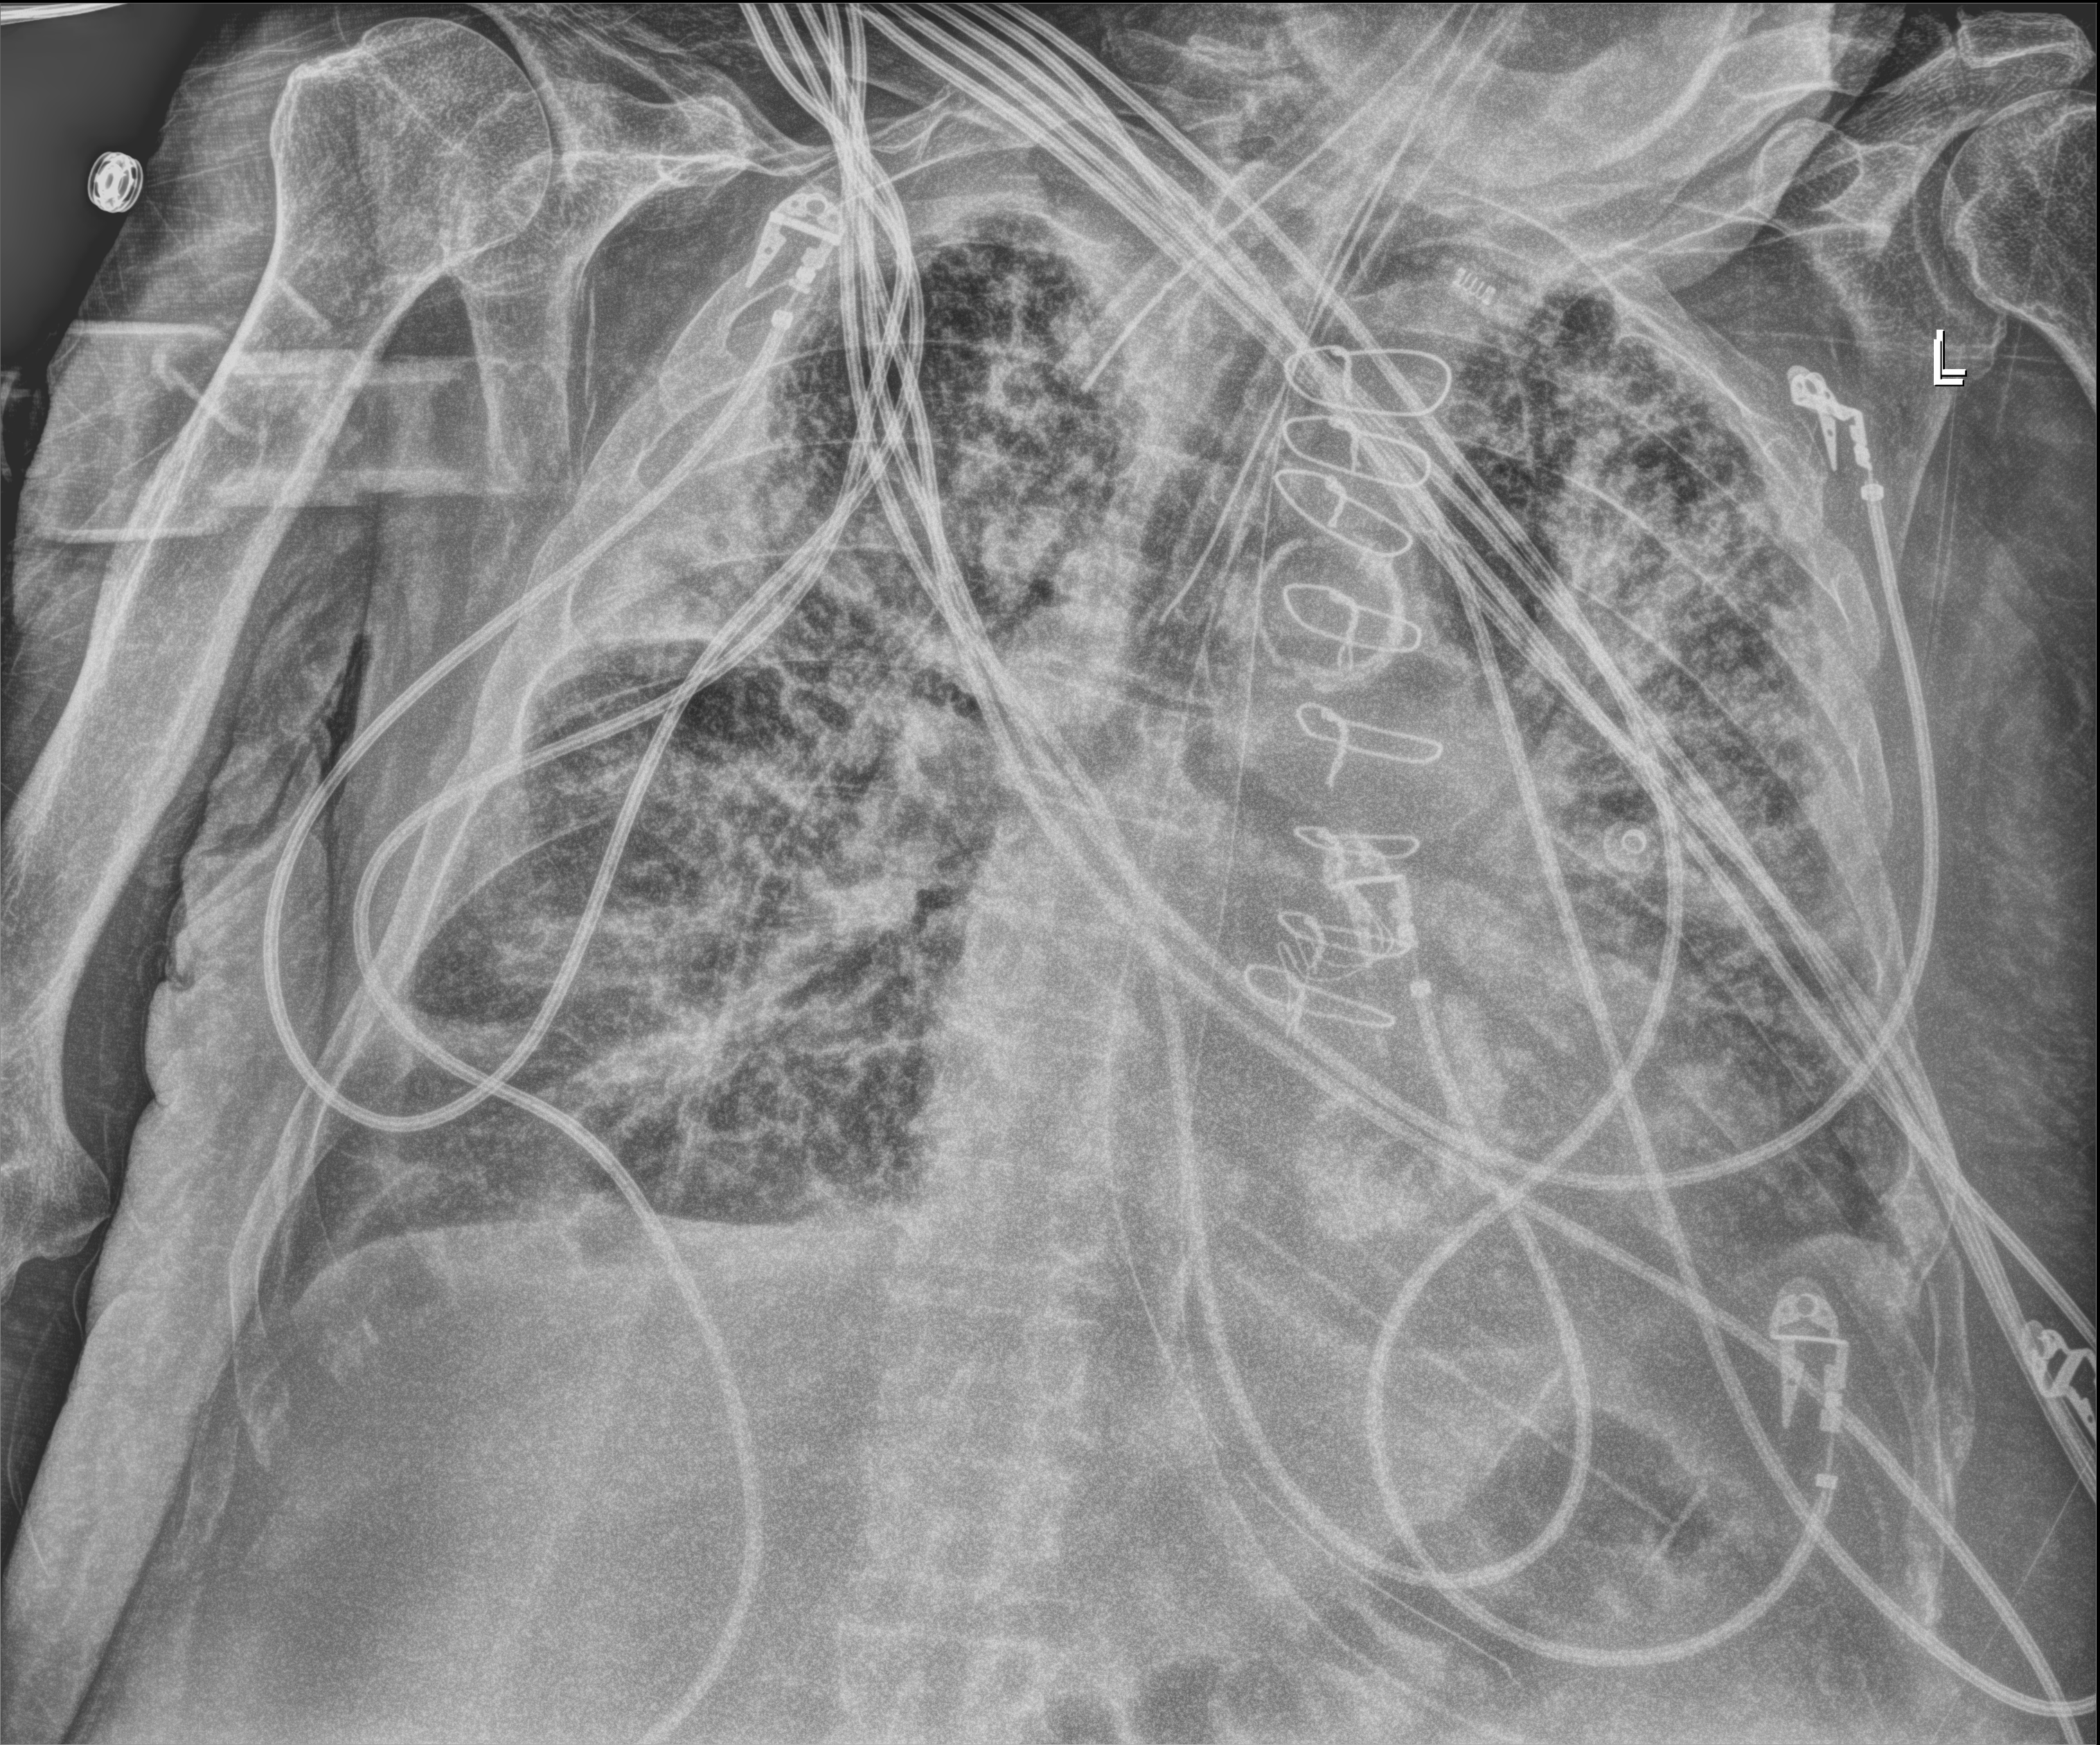
Chest X-ray (portable), anteroposterior (AP) projection. Male patient hospitalised with COVID-19, age 75–90 years.
From the hospital-stay record, not from the radiograph (when in the stay this image was taken is not recorded): mechanically ventilated during this hospital stay: yes; admitted to intensive care during this hospital stay: yes.